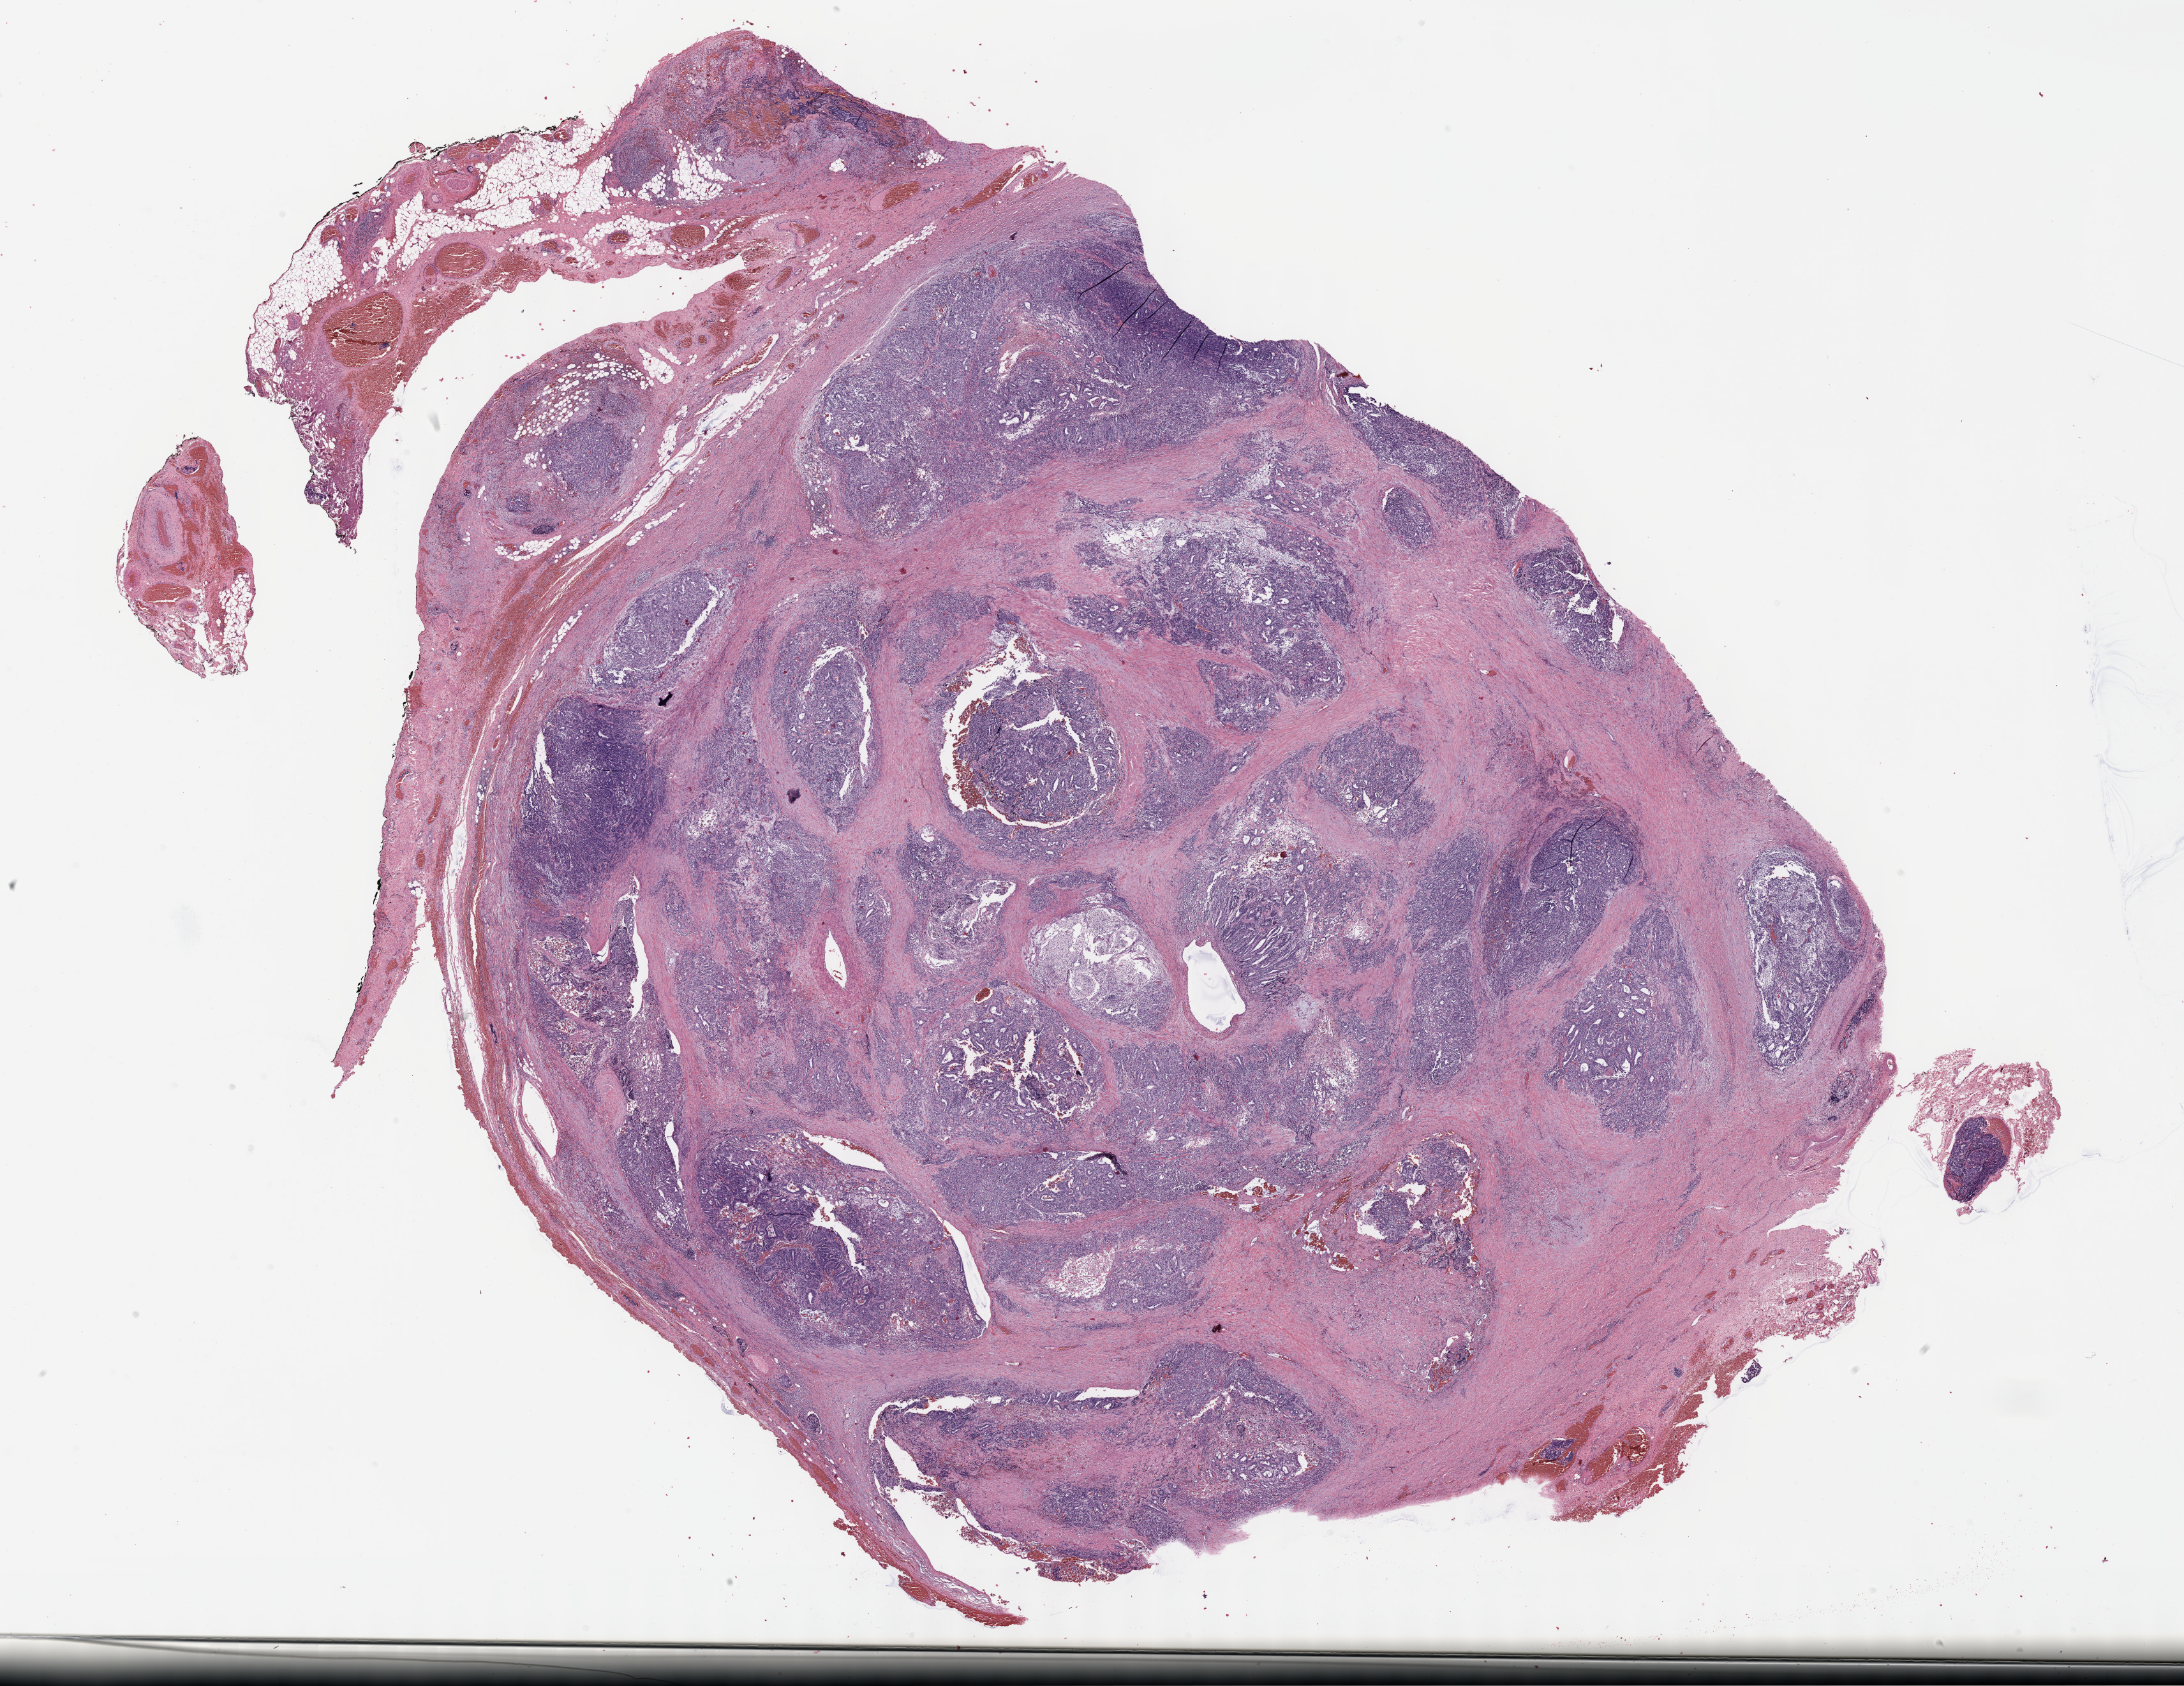
Whole-slide histology image, H&E-stained — whole scanned area (about 27.7 x 21.4 mm, slide scanned at 40x) shown as a low-resolution overview, formalin-fixed paraffin-embedded (FFPE) diagnostic section, testis, primary tumour sample. Male patient; age at initial diagnosis 28 years.
Laterality: right. AJCC pathologic stage: IIIB. Pathologic diagnosis: Teratoma, malignant, NOS.